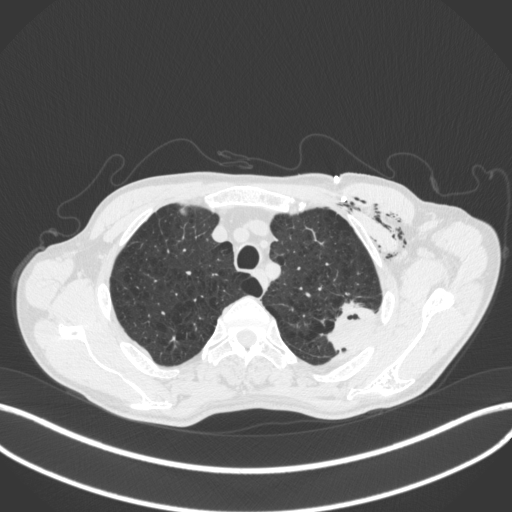
Chest CT, one axial slice; slice 340 of 416 in the series (ordered by position); lung window (W 1500 / L -600 HU); 512 × 512 image matrix. Patient: male, 58 years. Case-level facts recorded for this patient, not image findings: clinical TNM (as recorded): T3 N0 M0.
Annotated regions visible in this slice (bounding box drawn by a radiologist):
- lung tumour (recorded histology: adenocarcinoma): box from (x=316, y=300) to (x=380, y=355) px